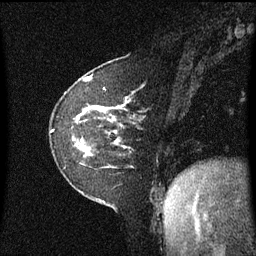
Breast MRI (dynamic contrast-enhanced), one sagittal slice; position 19 of 60 along the scan axis; dynamic contrast-enhanced series, image 2 of 3 at this slice position (ordered by acquisition); 1.5 T; TE 4.2 ms, TR 8.4 ms; 256 × 256 image matrix, field of view 210 × 210 mm. Female patient, age 60 years. From the clinical record (not read from this slice): setting: breast cancer imaged before/during neoadjuvant chemotherapy; receptor status: triple-negative.
Structures marked on this image (semi-automatically segmented with operator editing):
- analysis volume of interest (the breast-tissue region the enhancement analysis was run in; not a lesion): bounding box <51,100,128,168> (left, top, right, bottom; pixels)
- tumour enhancement mask (voxels above the 70 % enhancement threshold inside the analysis volume of interest): <84,107,118,144>